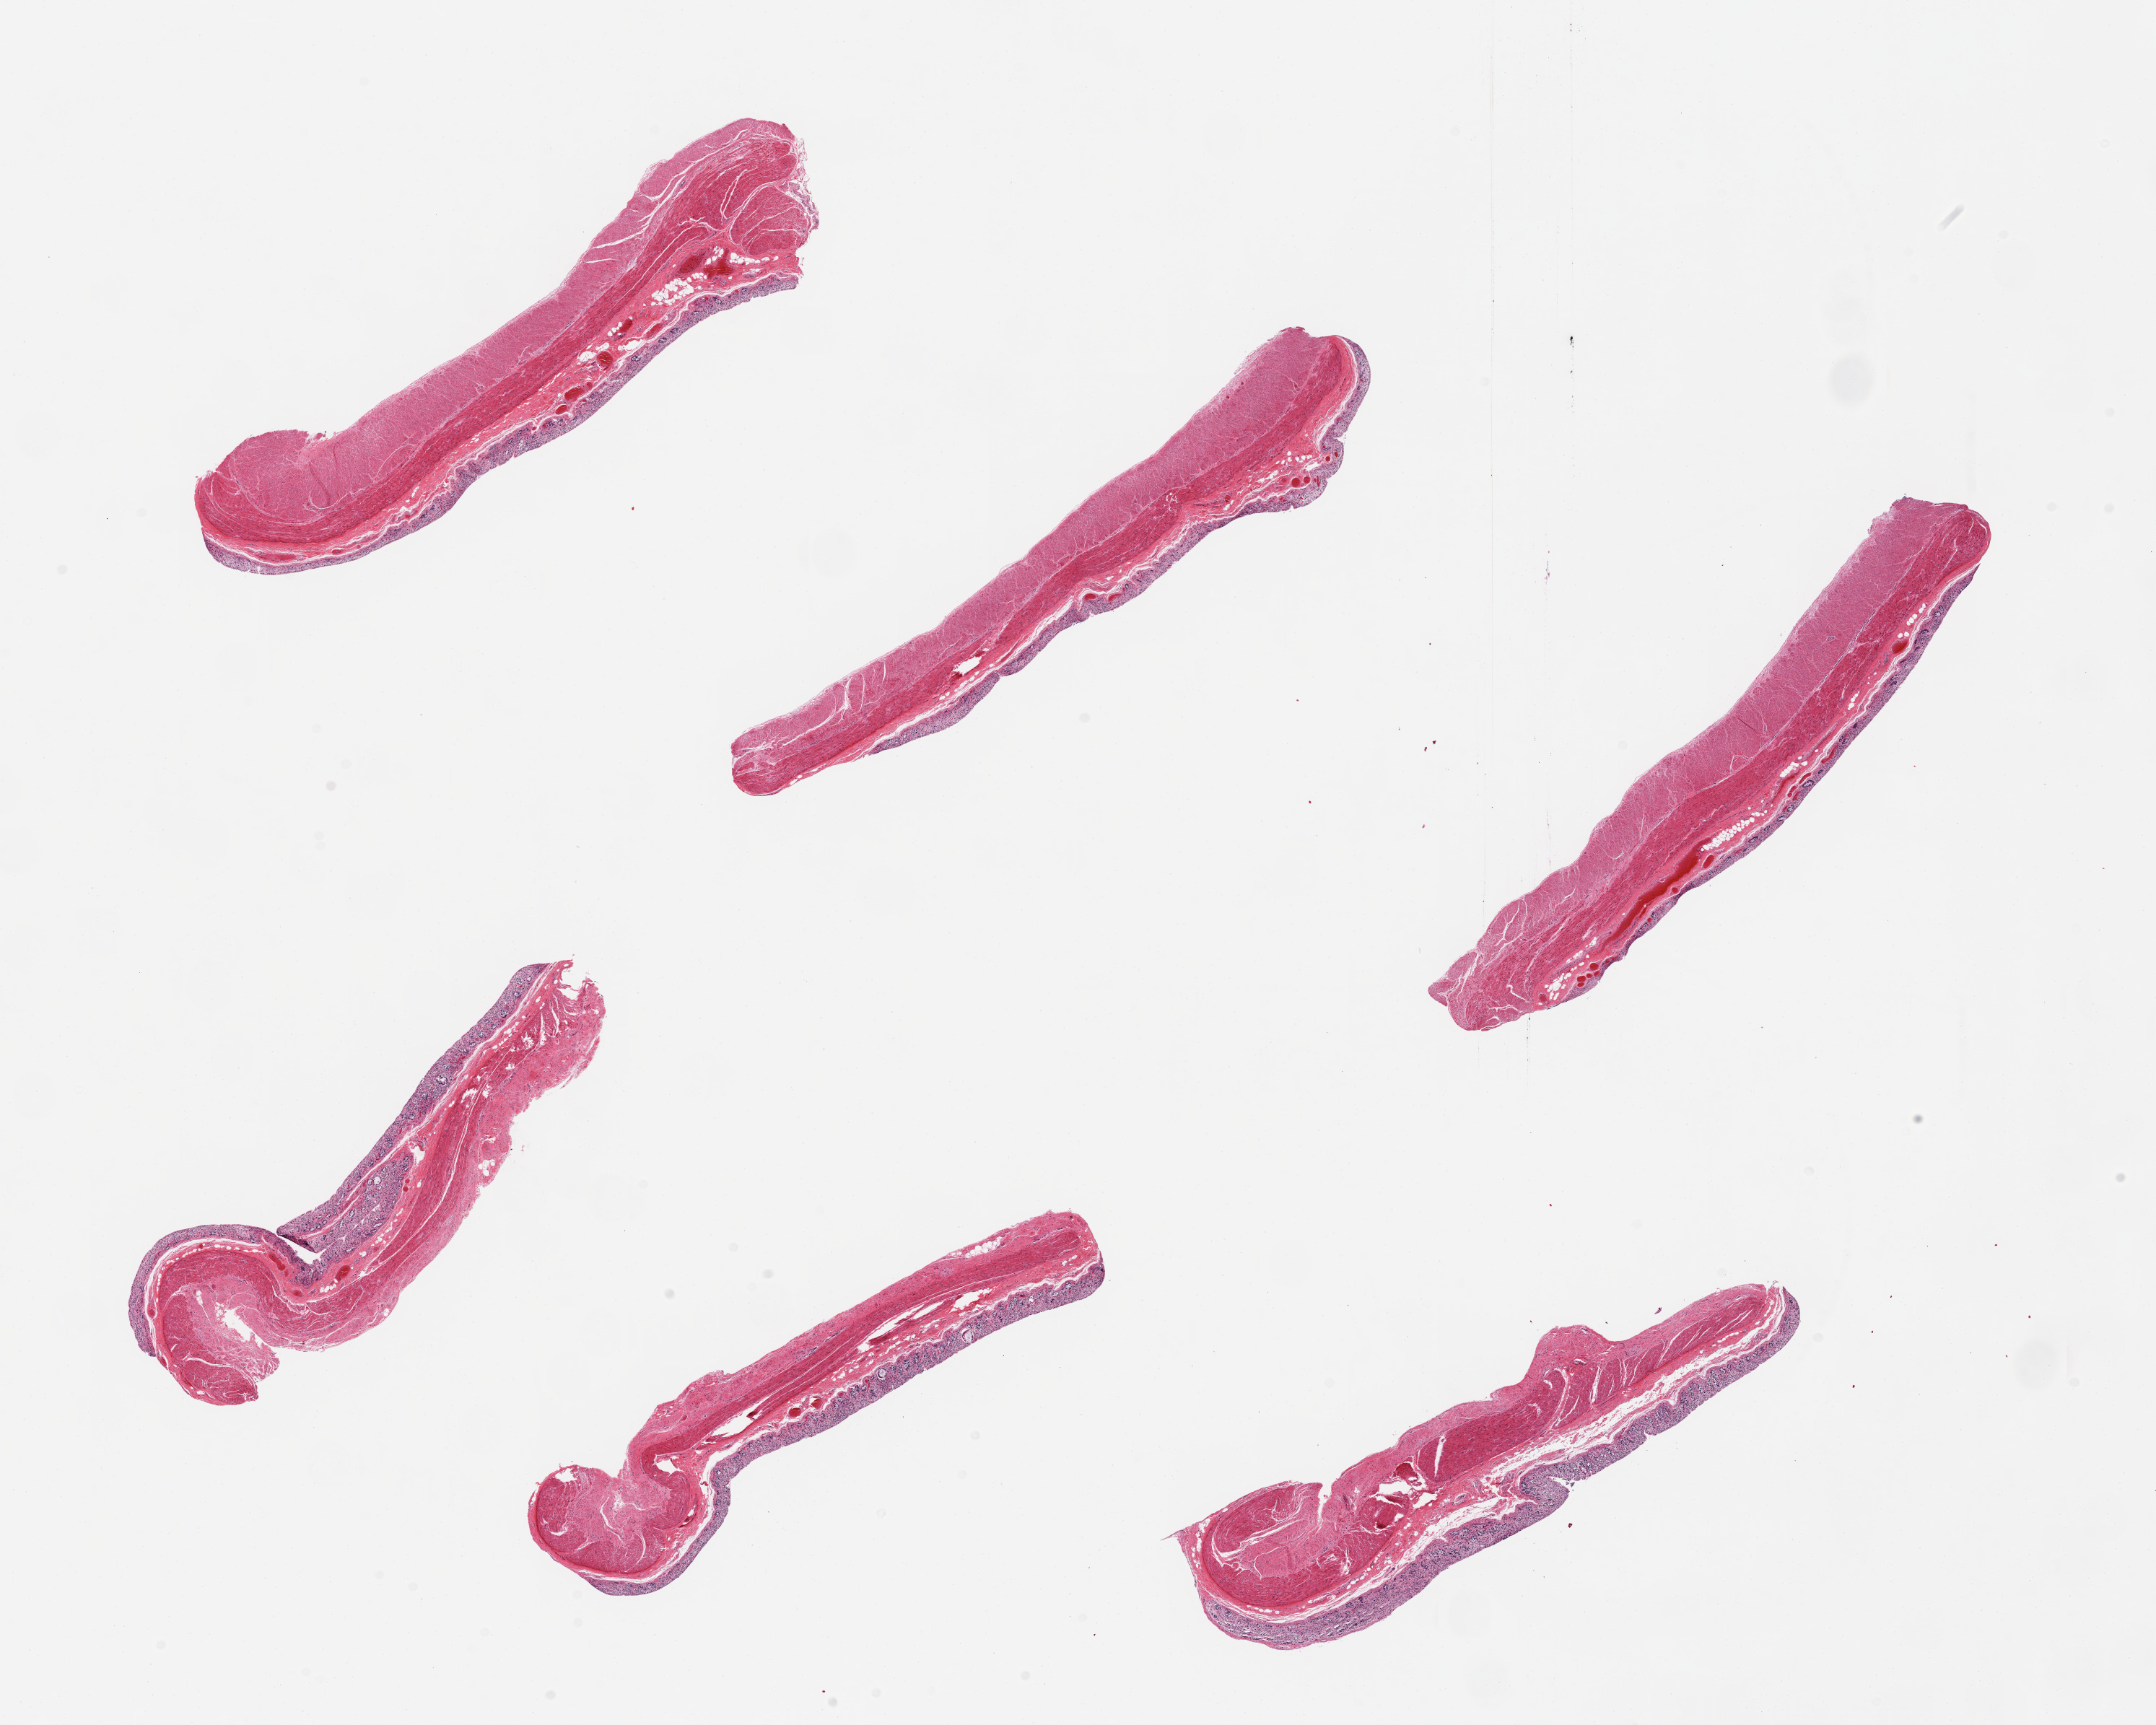
Whole-slide image, H&E stain, brightfield, shown as a low-resolution overview of the whole scanned area (about 23.6 x 18.9 mm, slide scanned at 20x); PAXgene-fixed paraffin-embedded (PFPE) section; sampled site (target tissue): transverse colon; tissue donor sample. Female donor.
Review note (as recorded): 6 pieces, mucosa up to ~0.25 mm, ~20% thickness, glandular component totally autolyzed.